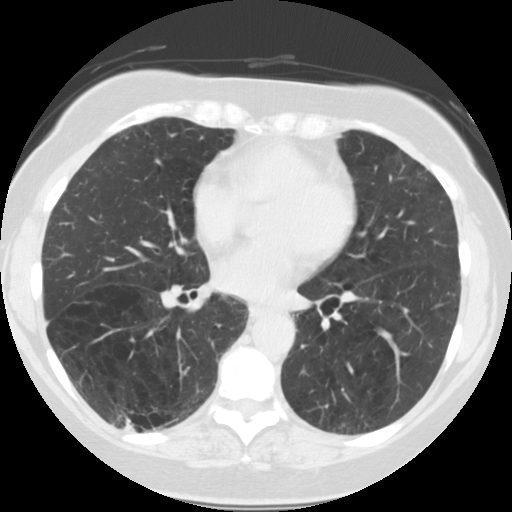
Chest CT (low-dose screening protocol), one axial image, first (baseline) screen, lung window (W 1500 / L -600 HU), standard (soft-tissue) reconstruction kernel (STANDARD), 140 kVp, slice 73 of 121 in the series. Female, age 59 years at enrolment. Current smoker at enrolment.
Expert reader's lesion annotation, bounding box <102,400,155,447> (left, top, right, bottom; pixels). No non-calcified nodule or mass ≥4 mm was recorded by the screening reader at this exam. Official screen result: negative screen, significant abnormalities not suspicious for lung cancer. Lung cancer was diagnosed 443 days after this screen (after the second annual screen): squamous cell carcinoma, NOS, right lower lobe, poorly differentiated (G3), stage IB (AJCC 6th edition), 30 mm at pathology.